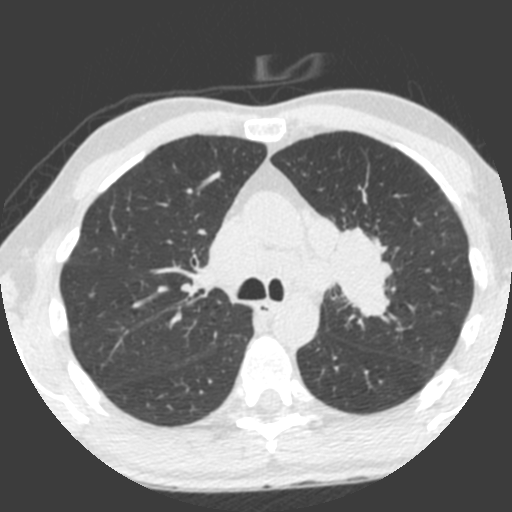
Low-dose screening chest CT, one axial slice; position 146 of 212 along the scan axis; 120 kVp; lung window (W 1500 / L -600 HU); 2 mm slice thickness; 512 × 512 image matrix, field of view 315 × 315 mm.
Outlined on this slice (outlined manually by an expert reader):
- lesion 1 (tumor, upper lobe of left lung): bounding box (x1, y1, x2, y2) in pixels: (329, 226, 393, 317)